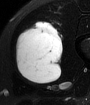
MRI of an extremity soft-tissue mass, one axial slice. Slice 26 of 65 in the series (ordered by position). T2-weighted fat-saturated. MR volume resampled by the dataset authors to the PET/CT grid (not the native acquisition matrix). 3.27 mm slice thickness. 90 × 105 image matrix, field of view 88 × 103 mm. Male patient. From the clinical record (not read from this slice): histological type: mixoid liposarcoma; grade: low; site of the primary tumour: left thigh.
Annotated regions visible in this slice (expert contour drawn on MRI and transferred to this co-registered scan by the dataset authors):
- gross tumour volume (mass): bounding box (x1, y1, x2, y2) in pixels: (14, 21, 63, 83)